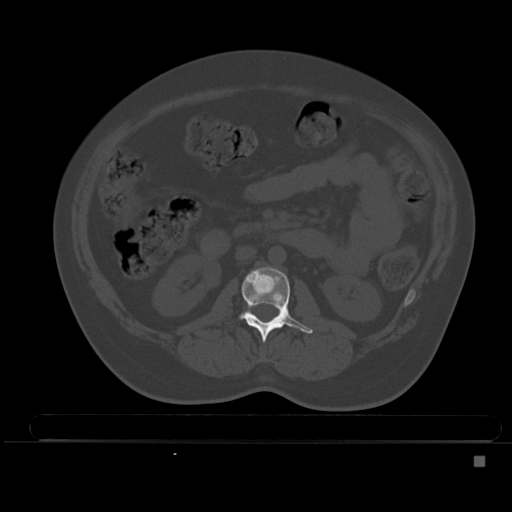
CT including the spine, one axial slice. Bone window (W 1800 / L 400 HU). 512 × 512 image matrix. Female patient, age 33 years. Case-level facts recorded for this patient, not image findings: primary cancer: breast; vertebrae with lytic lesions (as recorded): T1.
Outlined on this slice (semi-automatically segmented with operator editing):
- L2 vertebra: bounding box [x1, y1, x2, y2] px = [239, 267, 313, 342]